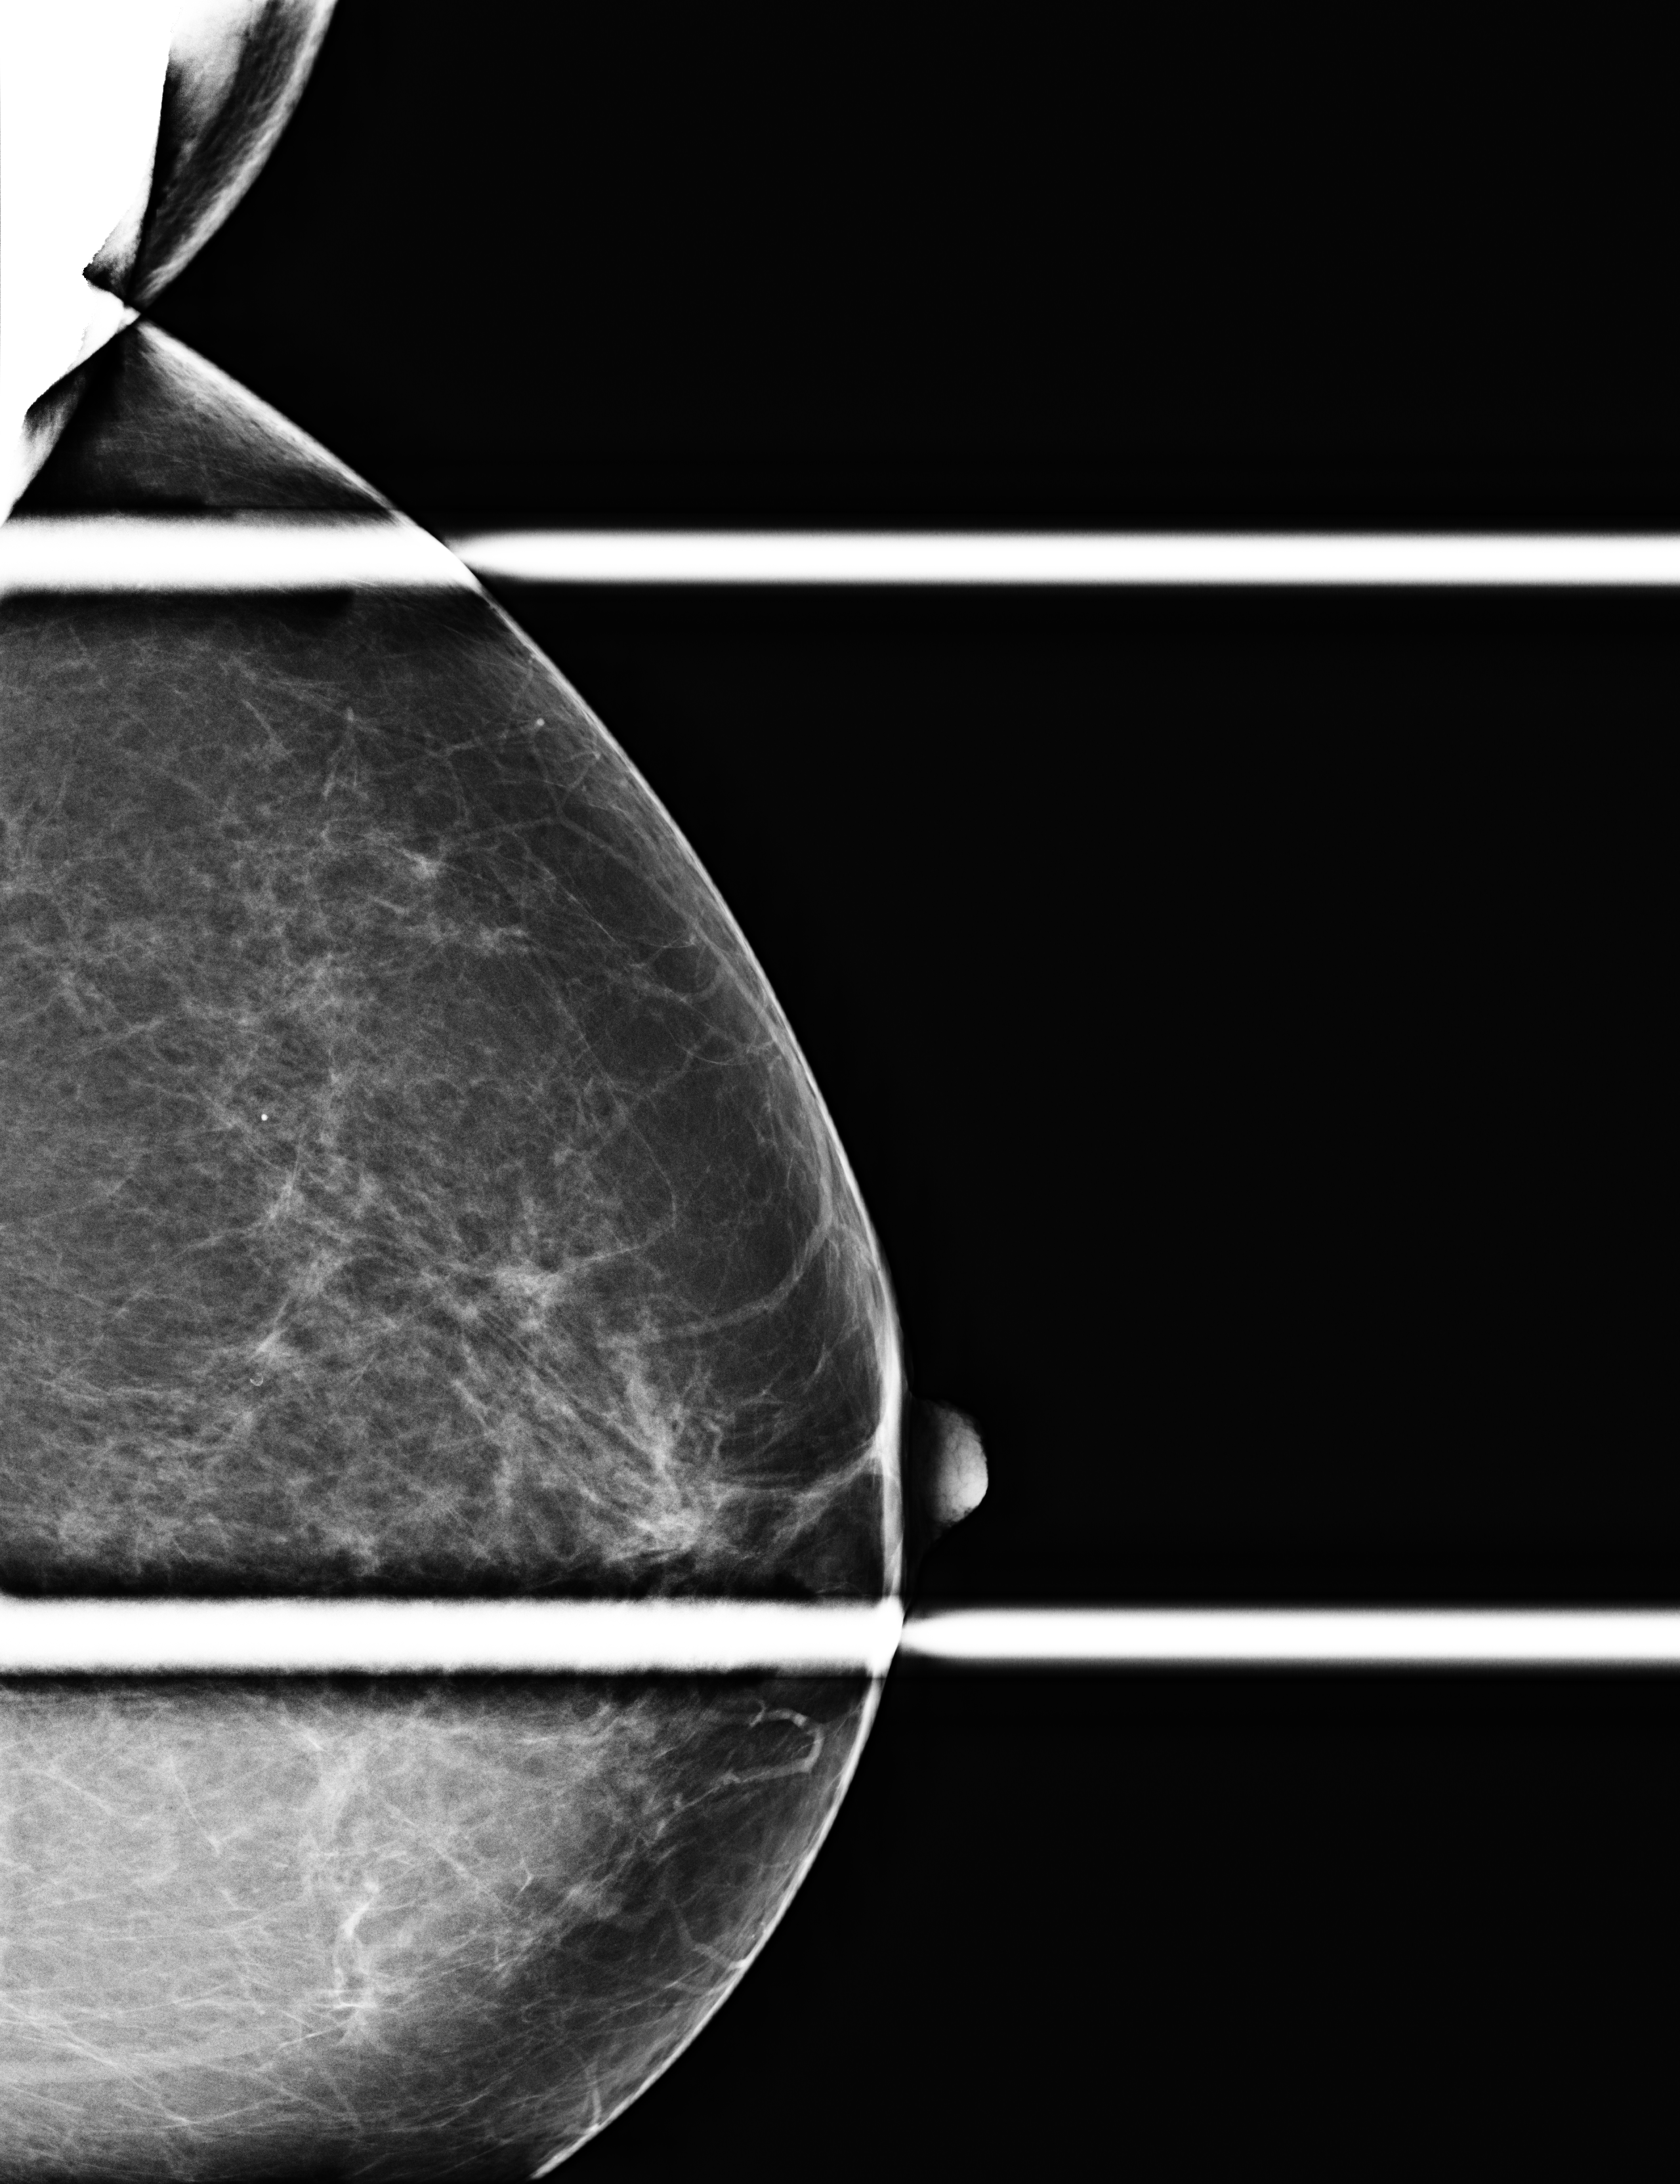
Digital mammogram (FFDM); left breast; CC view (spot compression); additional work-up view; compressed breast thickness 61 mm. Female patient, age 74 years.
BI-RADS breast density category at the screening exam (both breasts, scale 1–4): 3. Final BI-RADS category for the screening round (tomosynthesis exam, both breasts): category 4. Recall: recalled for additional imaging after this screen.